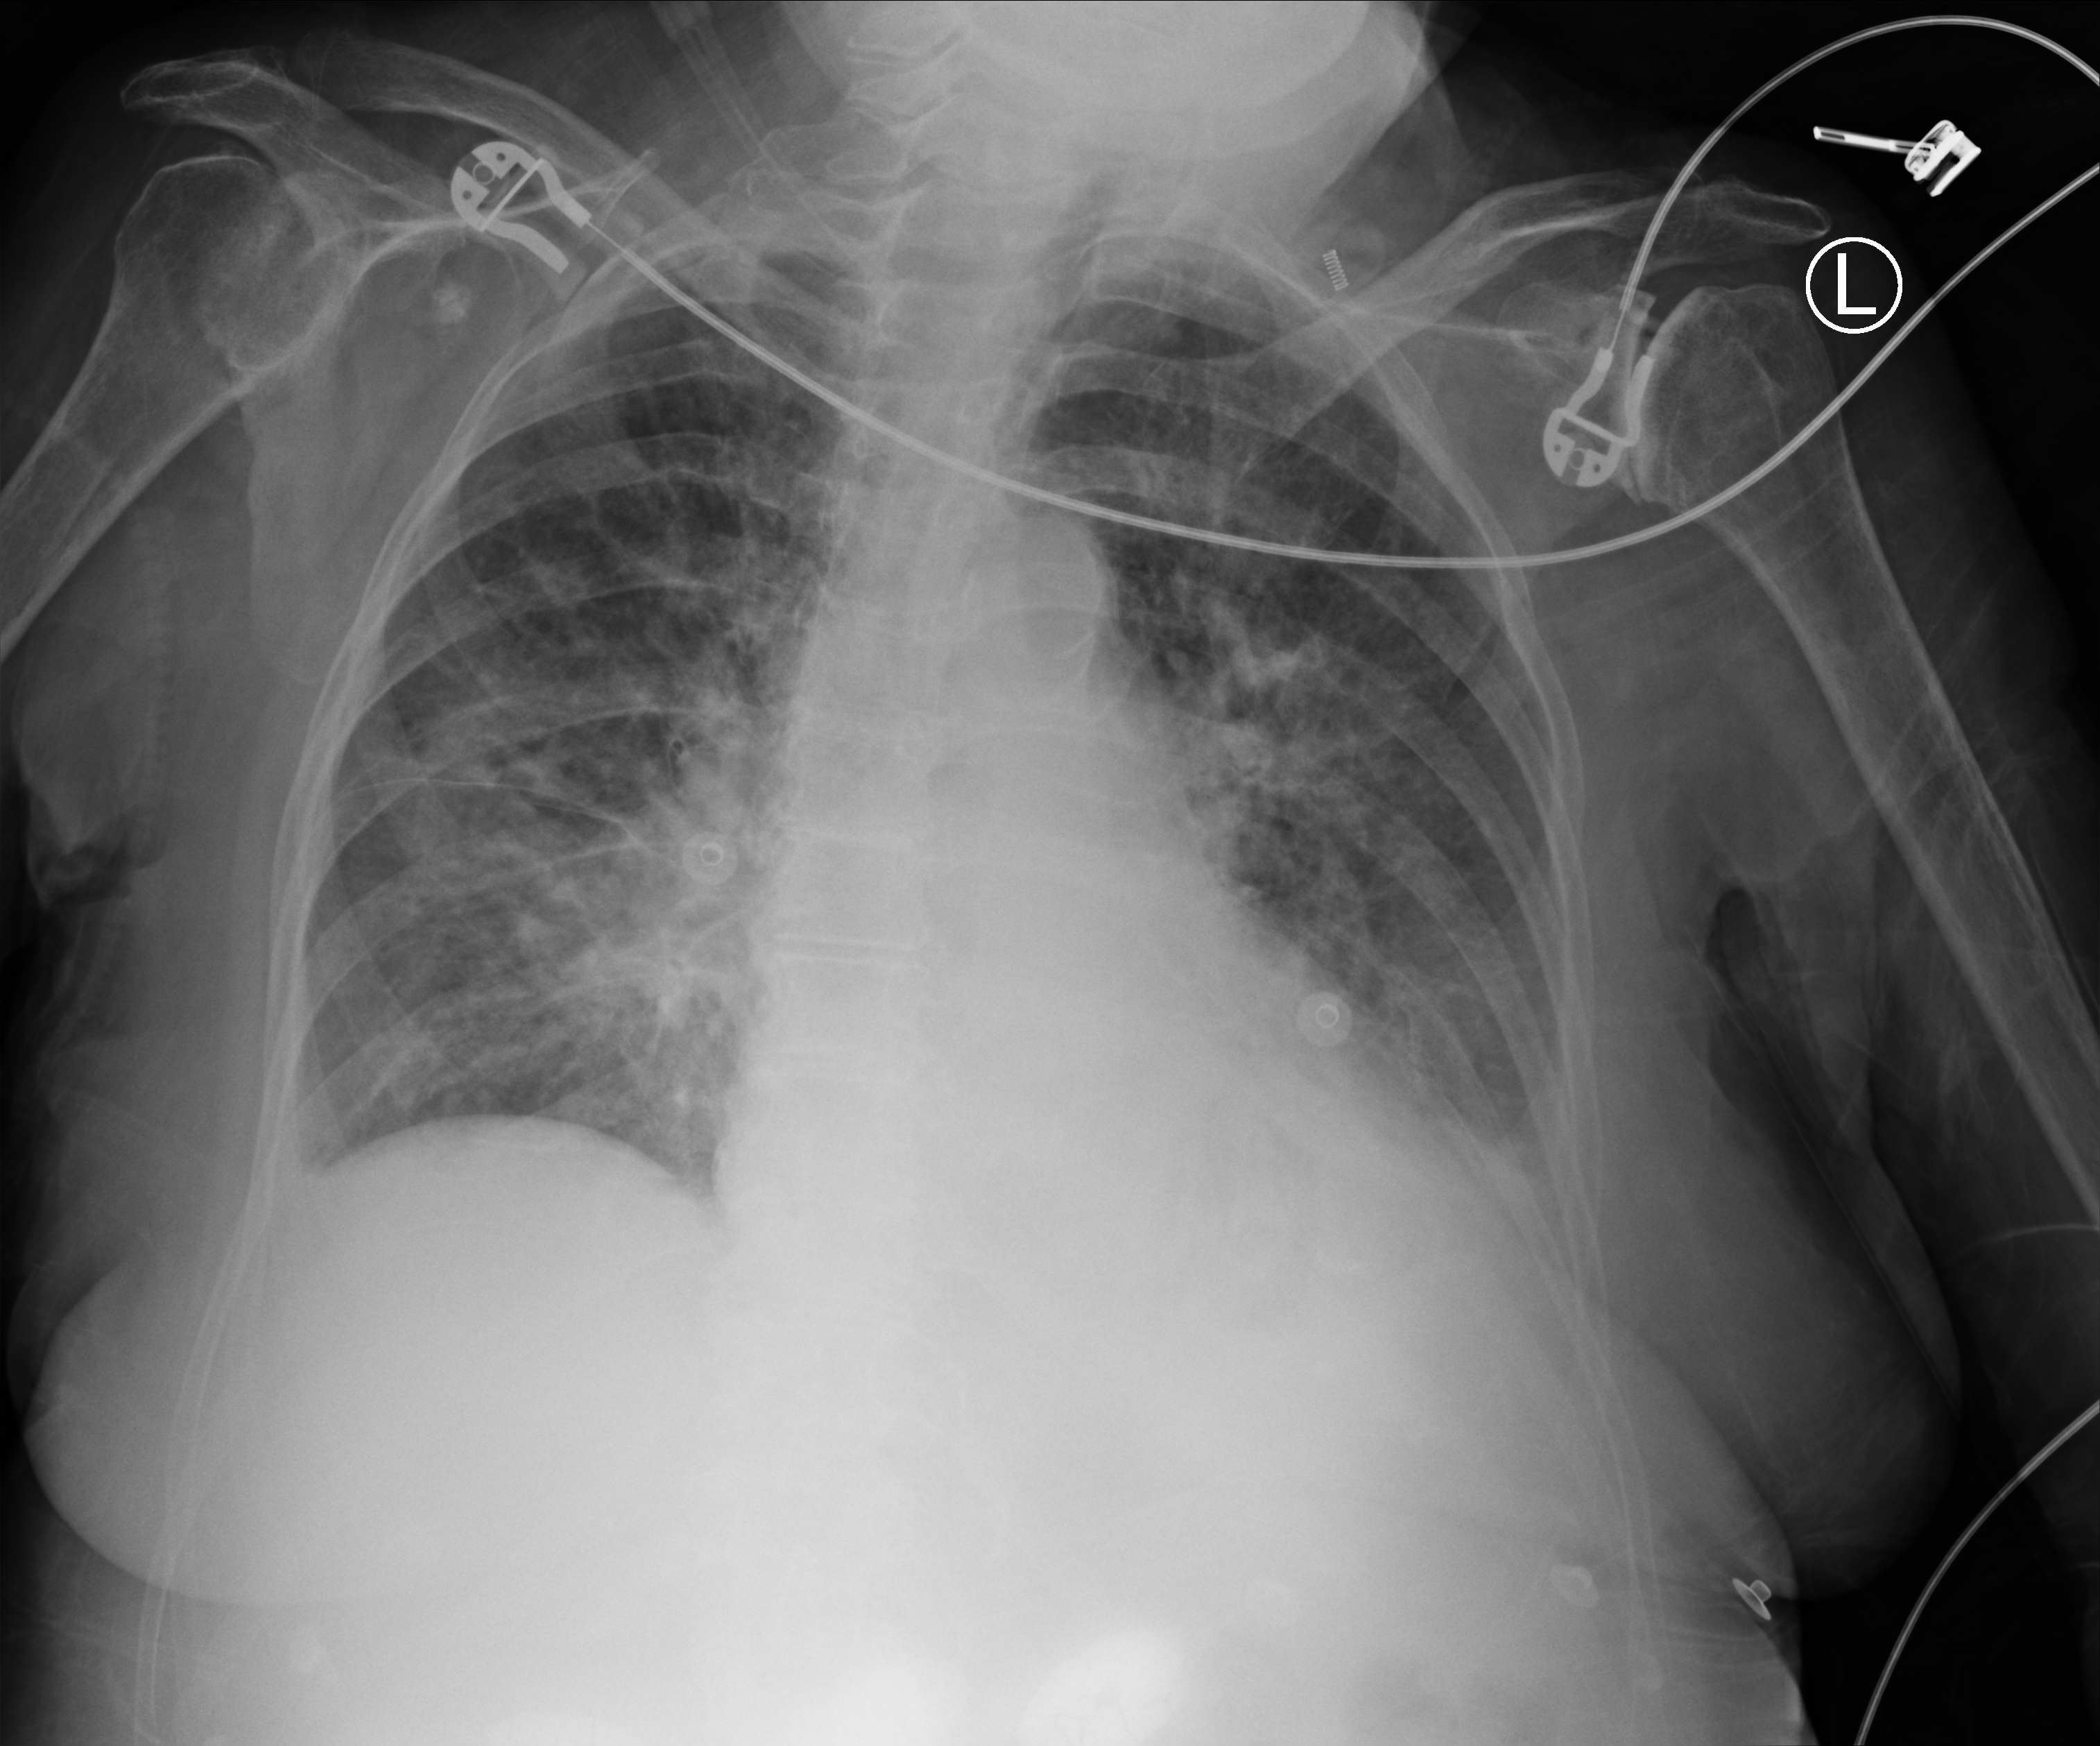
Chest X-ray (portable), anteroposterior (AP) projection. Patient hospitalised with COVID-19; female, aged 75–90 years.
Admission-level facts for this patient (not findings on this image; timing relative to this image not recorded): mechanically ventilated during this hospital stay: no; length of hospital stay: 9 days.